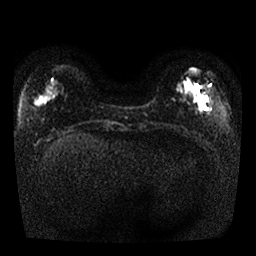
Breast MRI, one axial slice. Slice 7 of 25 in the series (ordered by position). Diffusion-weighted series; image 2 of 4 stored at this slice position (different b-values; order by instance number). 1.5 T. 256 × 256 image matrix. Female patient.
Outlined on this slice (outlined manually by an expert reader):
- tumour on diffusion-weighted imaging: box from (x=187, y=82) to (x=198, y=95) px